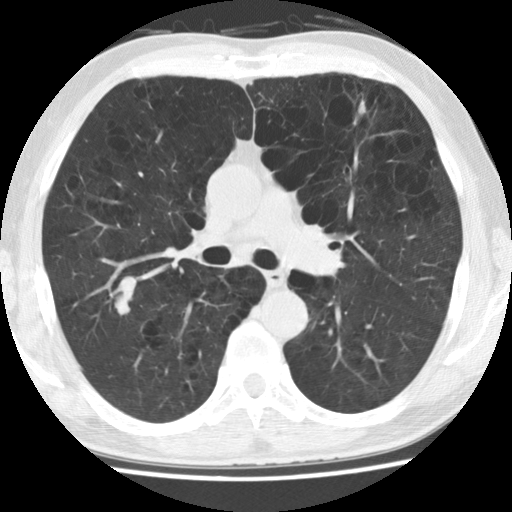
Axial slice from a low-dose chest CT screening exam; baseline screening round; lung window (W 1500 / L -600 HU); 2.5 mm slice thickness; 512 × 512 image matrix, field of view 324 × 324 mm. Male, age 62 years at enrolment.
- Lesion marked by an expert reader, bounding box (x1, y1, x2, y2) in pixels: (93, 263, 149, 325).
- The screening reader recorded 2 non-calcified nodules or masses ≥4 mm on this exam; which of them this box marks is not recorded.